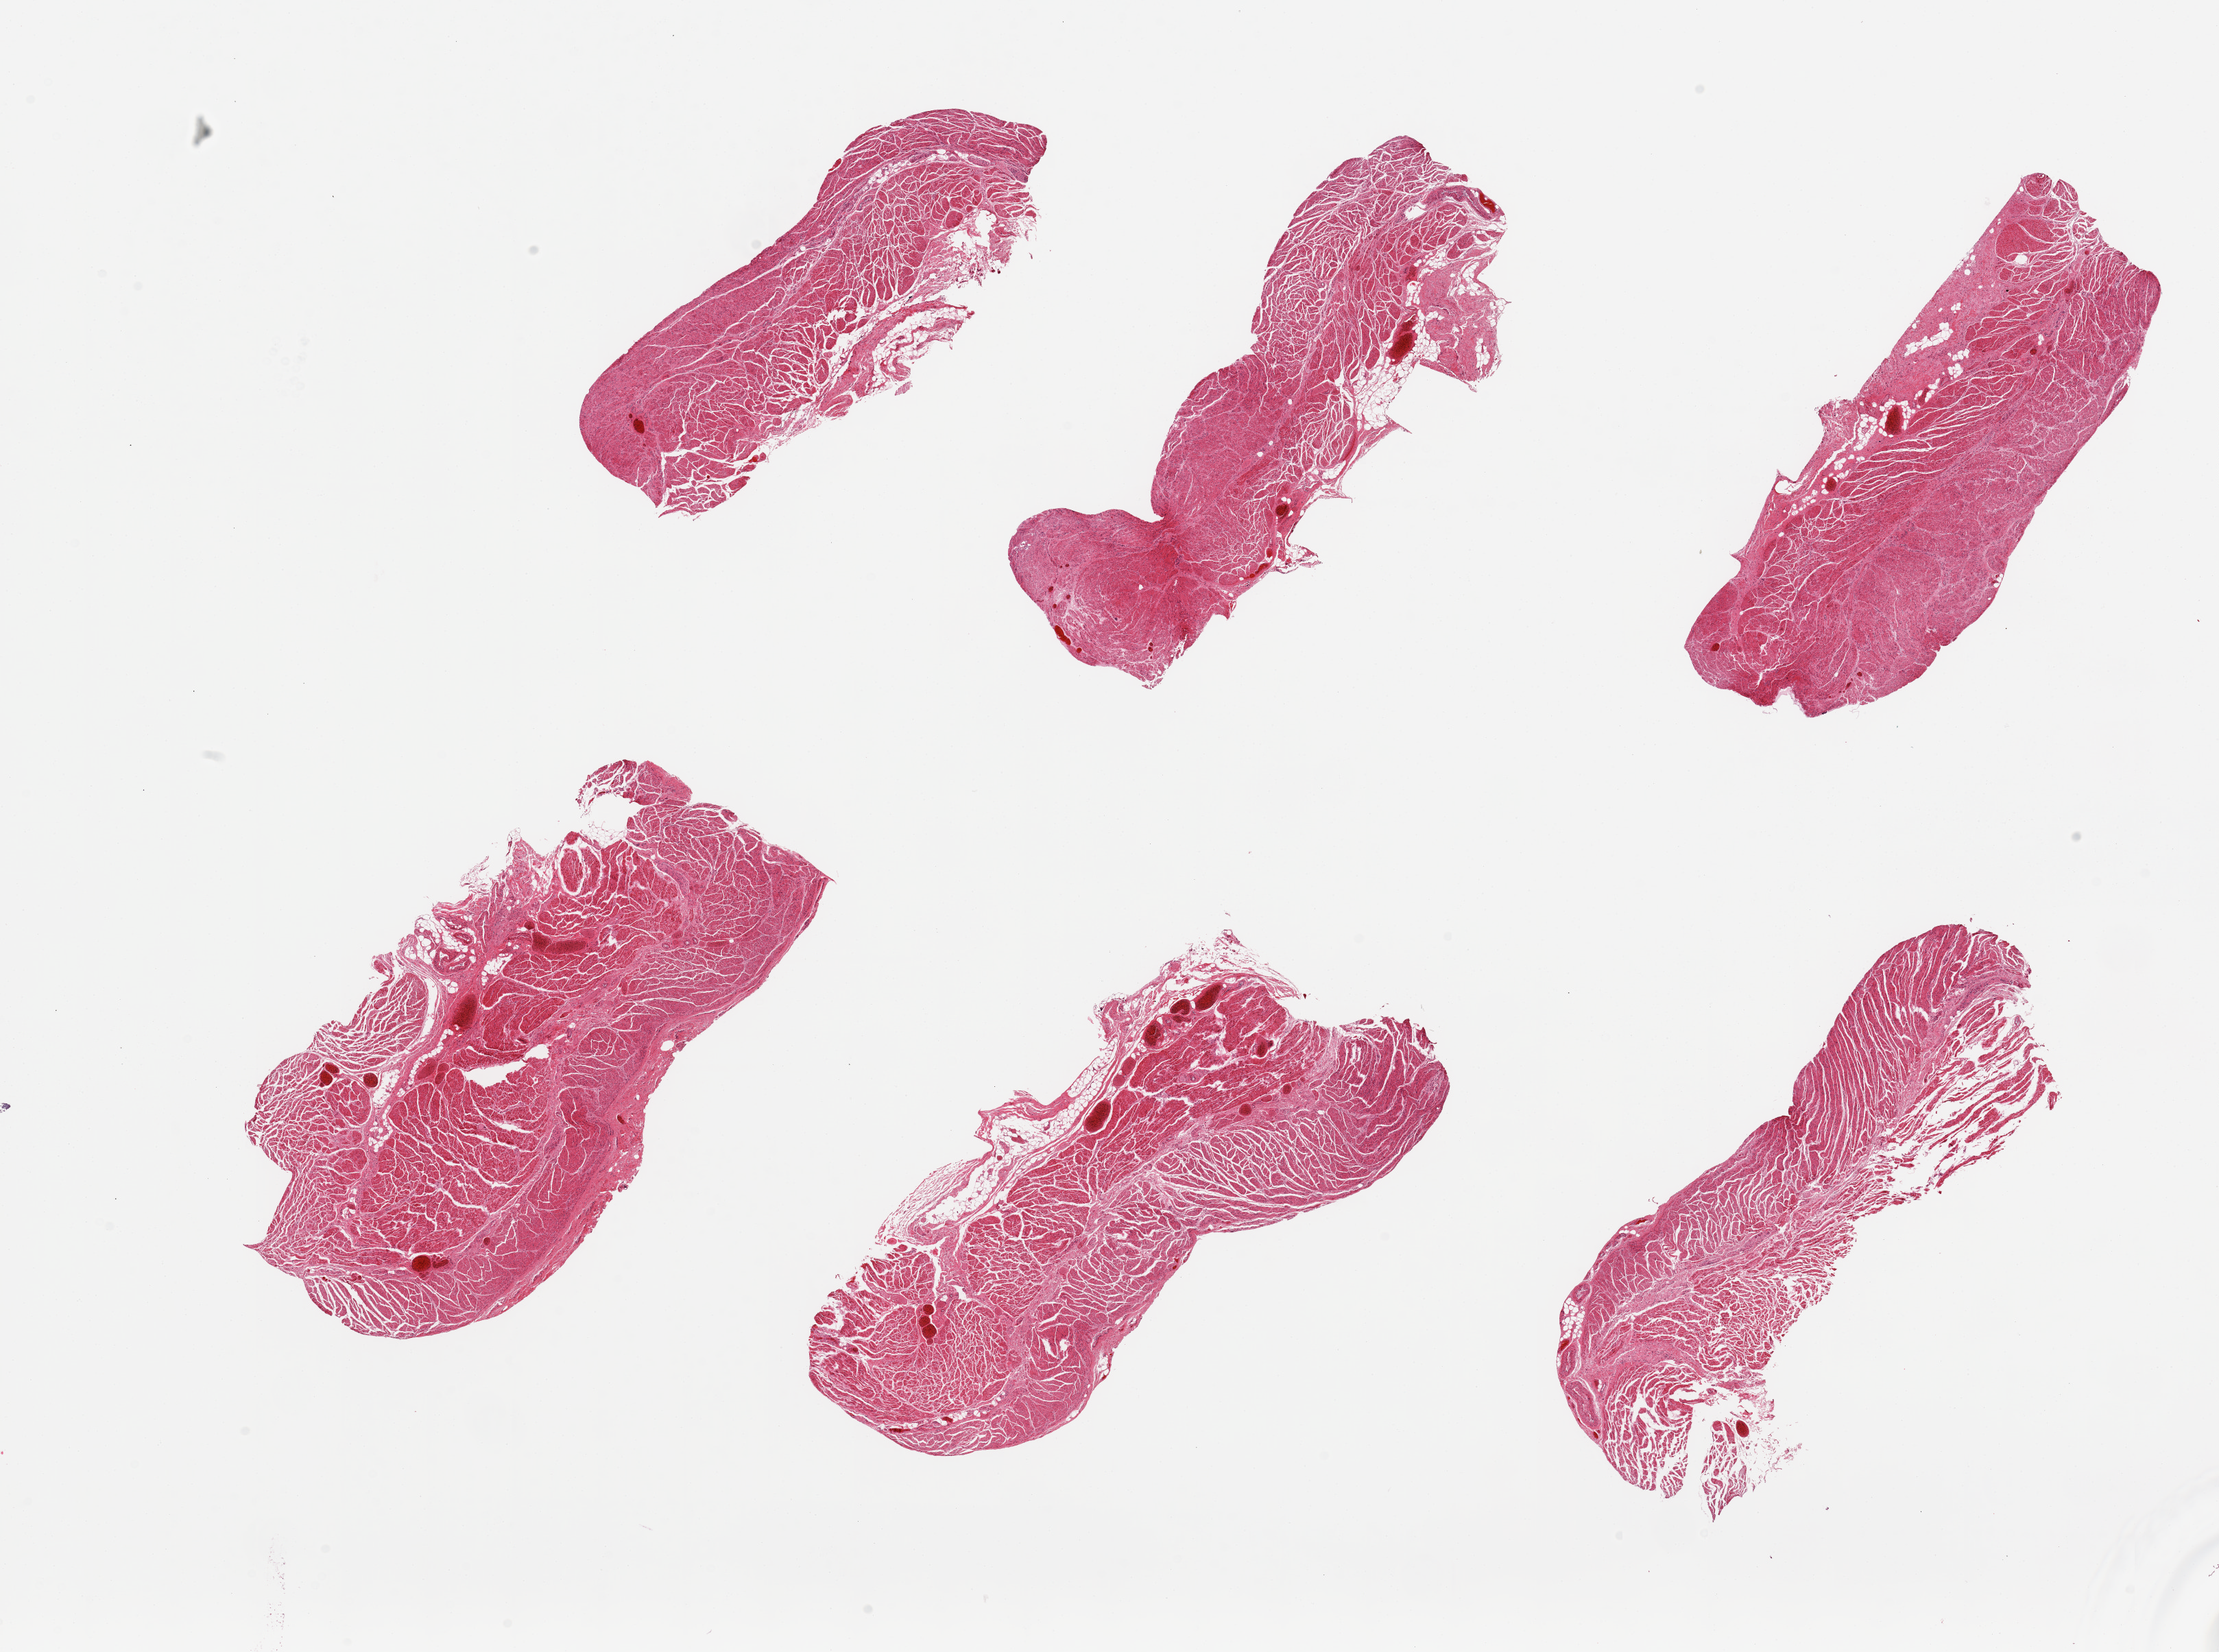
Whole-slide image, H&E stain — whole scanned area (about 25.6 x 19.1 mm, from a 20x scan) shown as a low-resolution overview. PAXgene-fixed paraffin-embedded (PFPE) section. Section of gastroesophageal junction (target tissue). Tissue donor sample. Donor: female.
• pathologist's review note for this sample: 6 pieces; well dissected